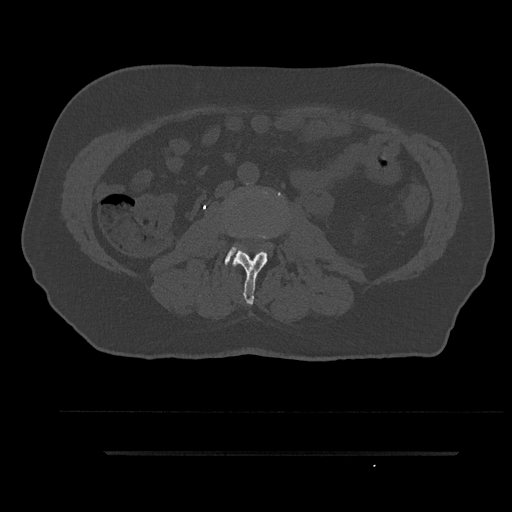
CT including the spine, one axial slice; slice 80 of 797 in the series (ordered by position); reconstruction kernel Br40s/3; 120 kVp; bone window (W 1800 / L 400 HU); 0.5 mm slice thickness; 512 × 512 image matrix. Patient: male, 63 years. From the clinical record (not read from this slice): primary cancer: renal; vertebrae with lytic lesions (as recorded): T8.
Structures marked on this image (semi-automatically segmented with operator editing):
- L2 vertebra: bounding box <232,234,269,305> (left, top, right, bottom; pixels)
- L3 vertebra: <225,194,281,265>